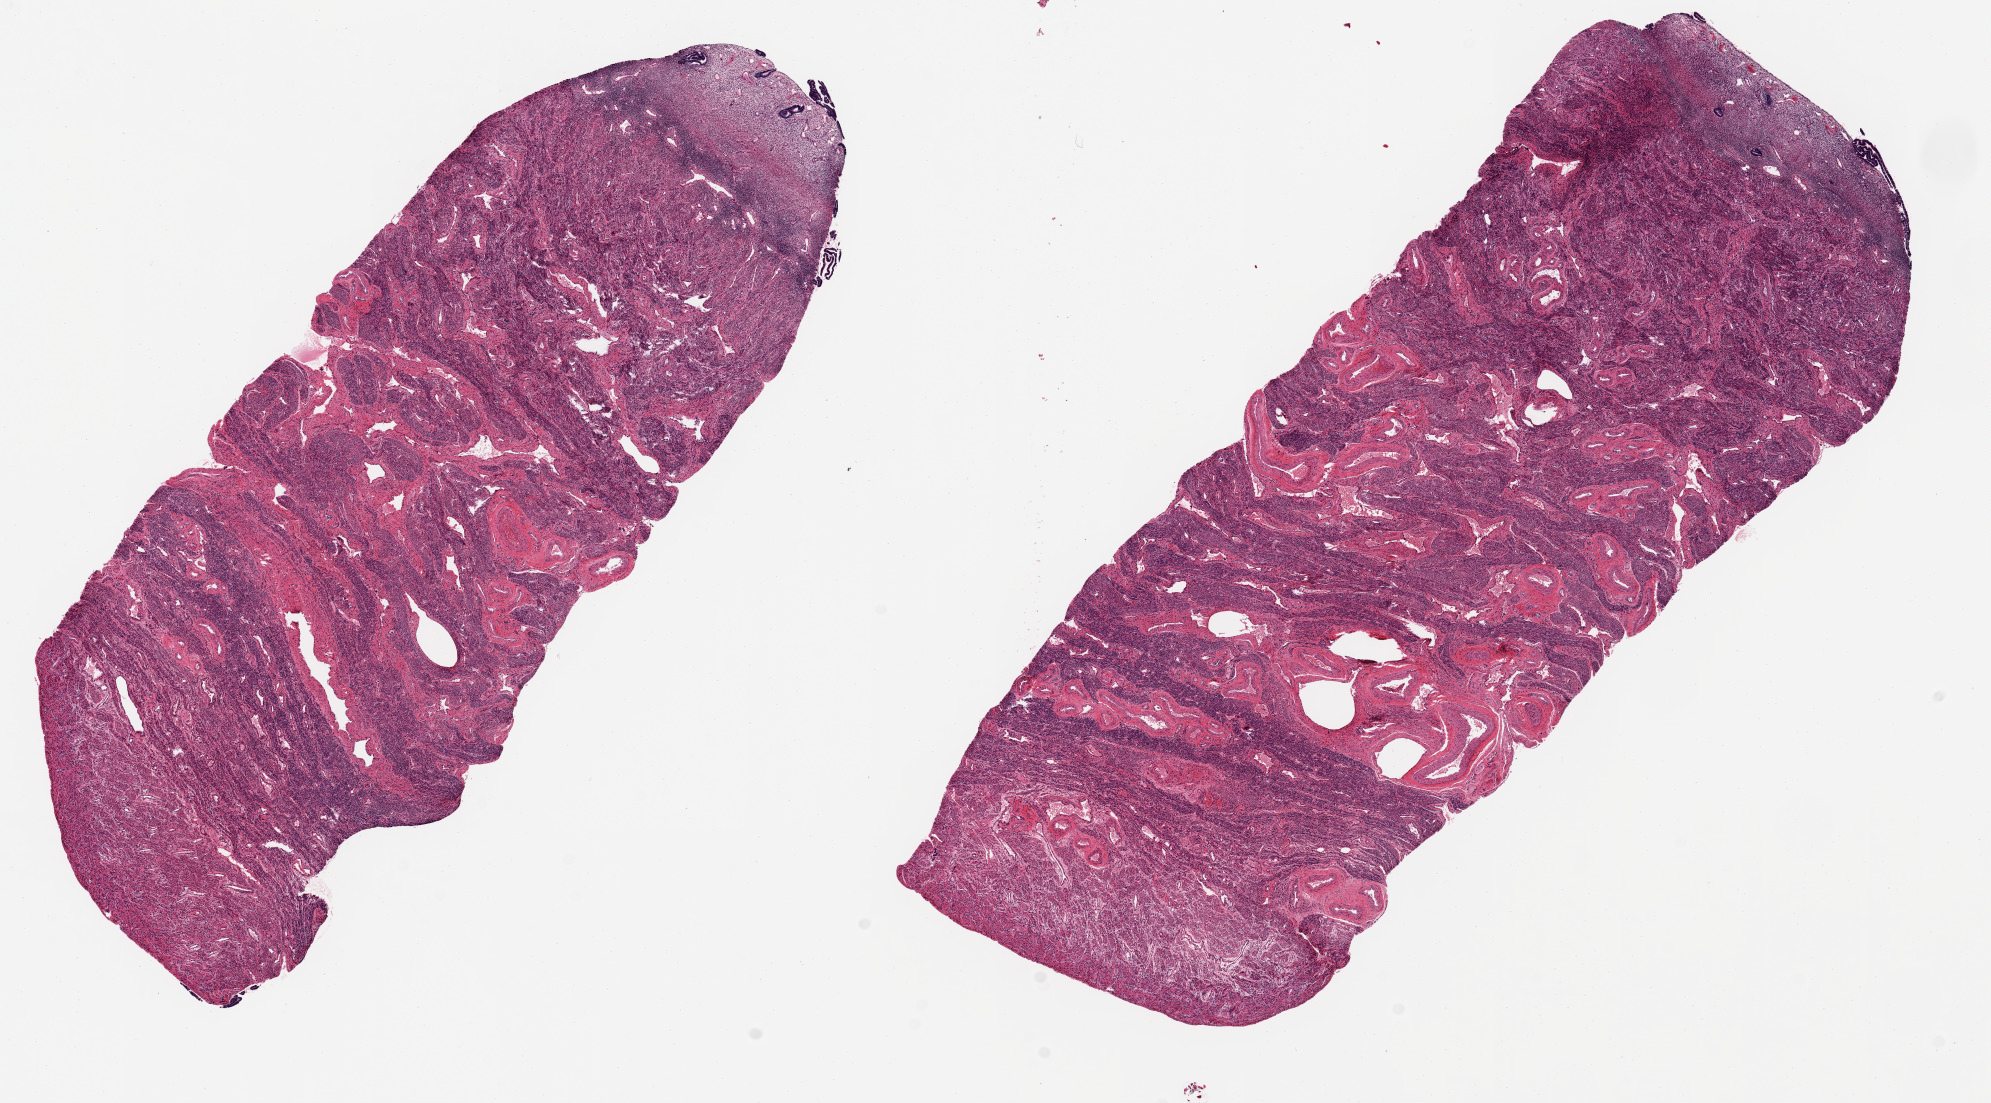
Digitized H&E-stained section, low-resolution overview of the scanned area, about 15.8 x 8.7 mm (acquisition: 20x scan). PAXgene-fixed, paraffin-embedded tissue. Target tissue: uterus. Tissue donor sample. Donor sex: female.
Reviewer comment on this tissue sample: 2 ~8.5x3mm aliquots. Autolyzed, atrophic endometrium is <10% of both.